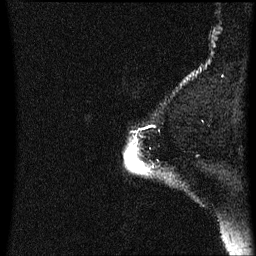
Breast MRI (dynamic contrast-enhanced), one sagittal slice; slice 57 of 60 in the series (ordered by position); dynamic contrast-enhanced series, image 2 of 3 at this slice position (ordered by acquisition); 1.5 T; TE 4.2 ms, TR 8.4 ms; 2 mm slice thickness; 256 × 256 image matrix, field of view 200 × 200 mm. Female patient, age 54 years. Case-level facts recorded for this patient, not image findings: setting: breast cancer imaged before/during neoadjuvant chemotherapy; receptor status: HR-positive, HER2-negative.
Outlined on this slice (semi-automatic segmentation, software-assisted and operator-edited):
- analysis volume of interest (the breast-tissue region the enhancement analysis was run in; not a lesion): box from (x=128, y=140) to (x=155, y=175) px
- tumour enhancement mask (voxels above the 70 % enhancement threshold inside the analysis volume of interest): (x=128, y=150)–(x=143, y=173)